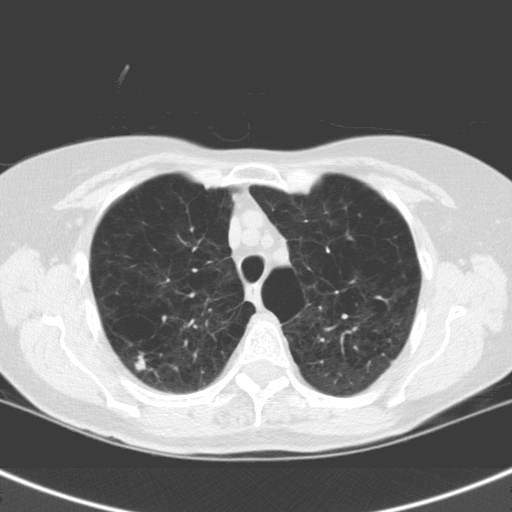
Low-dose screening chest CT, one axial slice. Slice 119 of 158 in the series (ordered by position). Lung window (W 1500 / L -600 HU). 3.2 mm slice thickness. 512 × 512 image matrix, field of view 301 × 301 mm.
Outlined on this slice (manually delineated by an expert):
- lesion 1 (tumor, upper lobe of right lung): bounding box <135,358,146,371> (left, top, right, bottom; pixels)